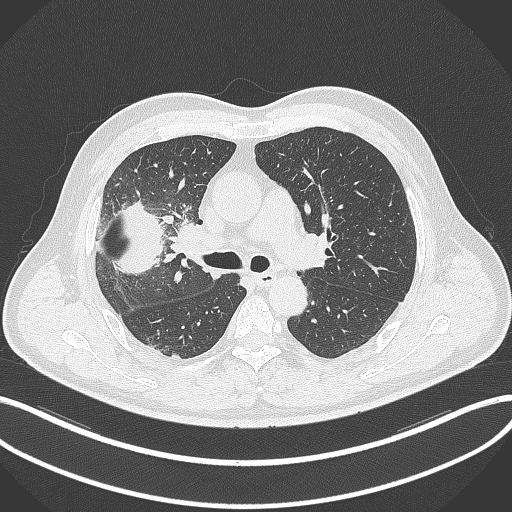
Chest CT, one axial slice; slice 207 of 348 in the series (ordered by position); 120 kVp; lung window (W 1500 / L -600 HU); 512 × 512 image matrix, field of view 400 × 400 mm. Male patient, age 55 years. Case-level facts recorded for this patient, not image findings: clinical TNM (as recorded): T3 N2 M1.
Outlined on this slice (bounding box drawn by a radiologist):
- lung tumour (recorded histology: adenocarcinoma): box from (x=101, y=201) to (x=166, y=279) px